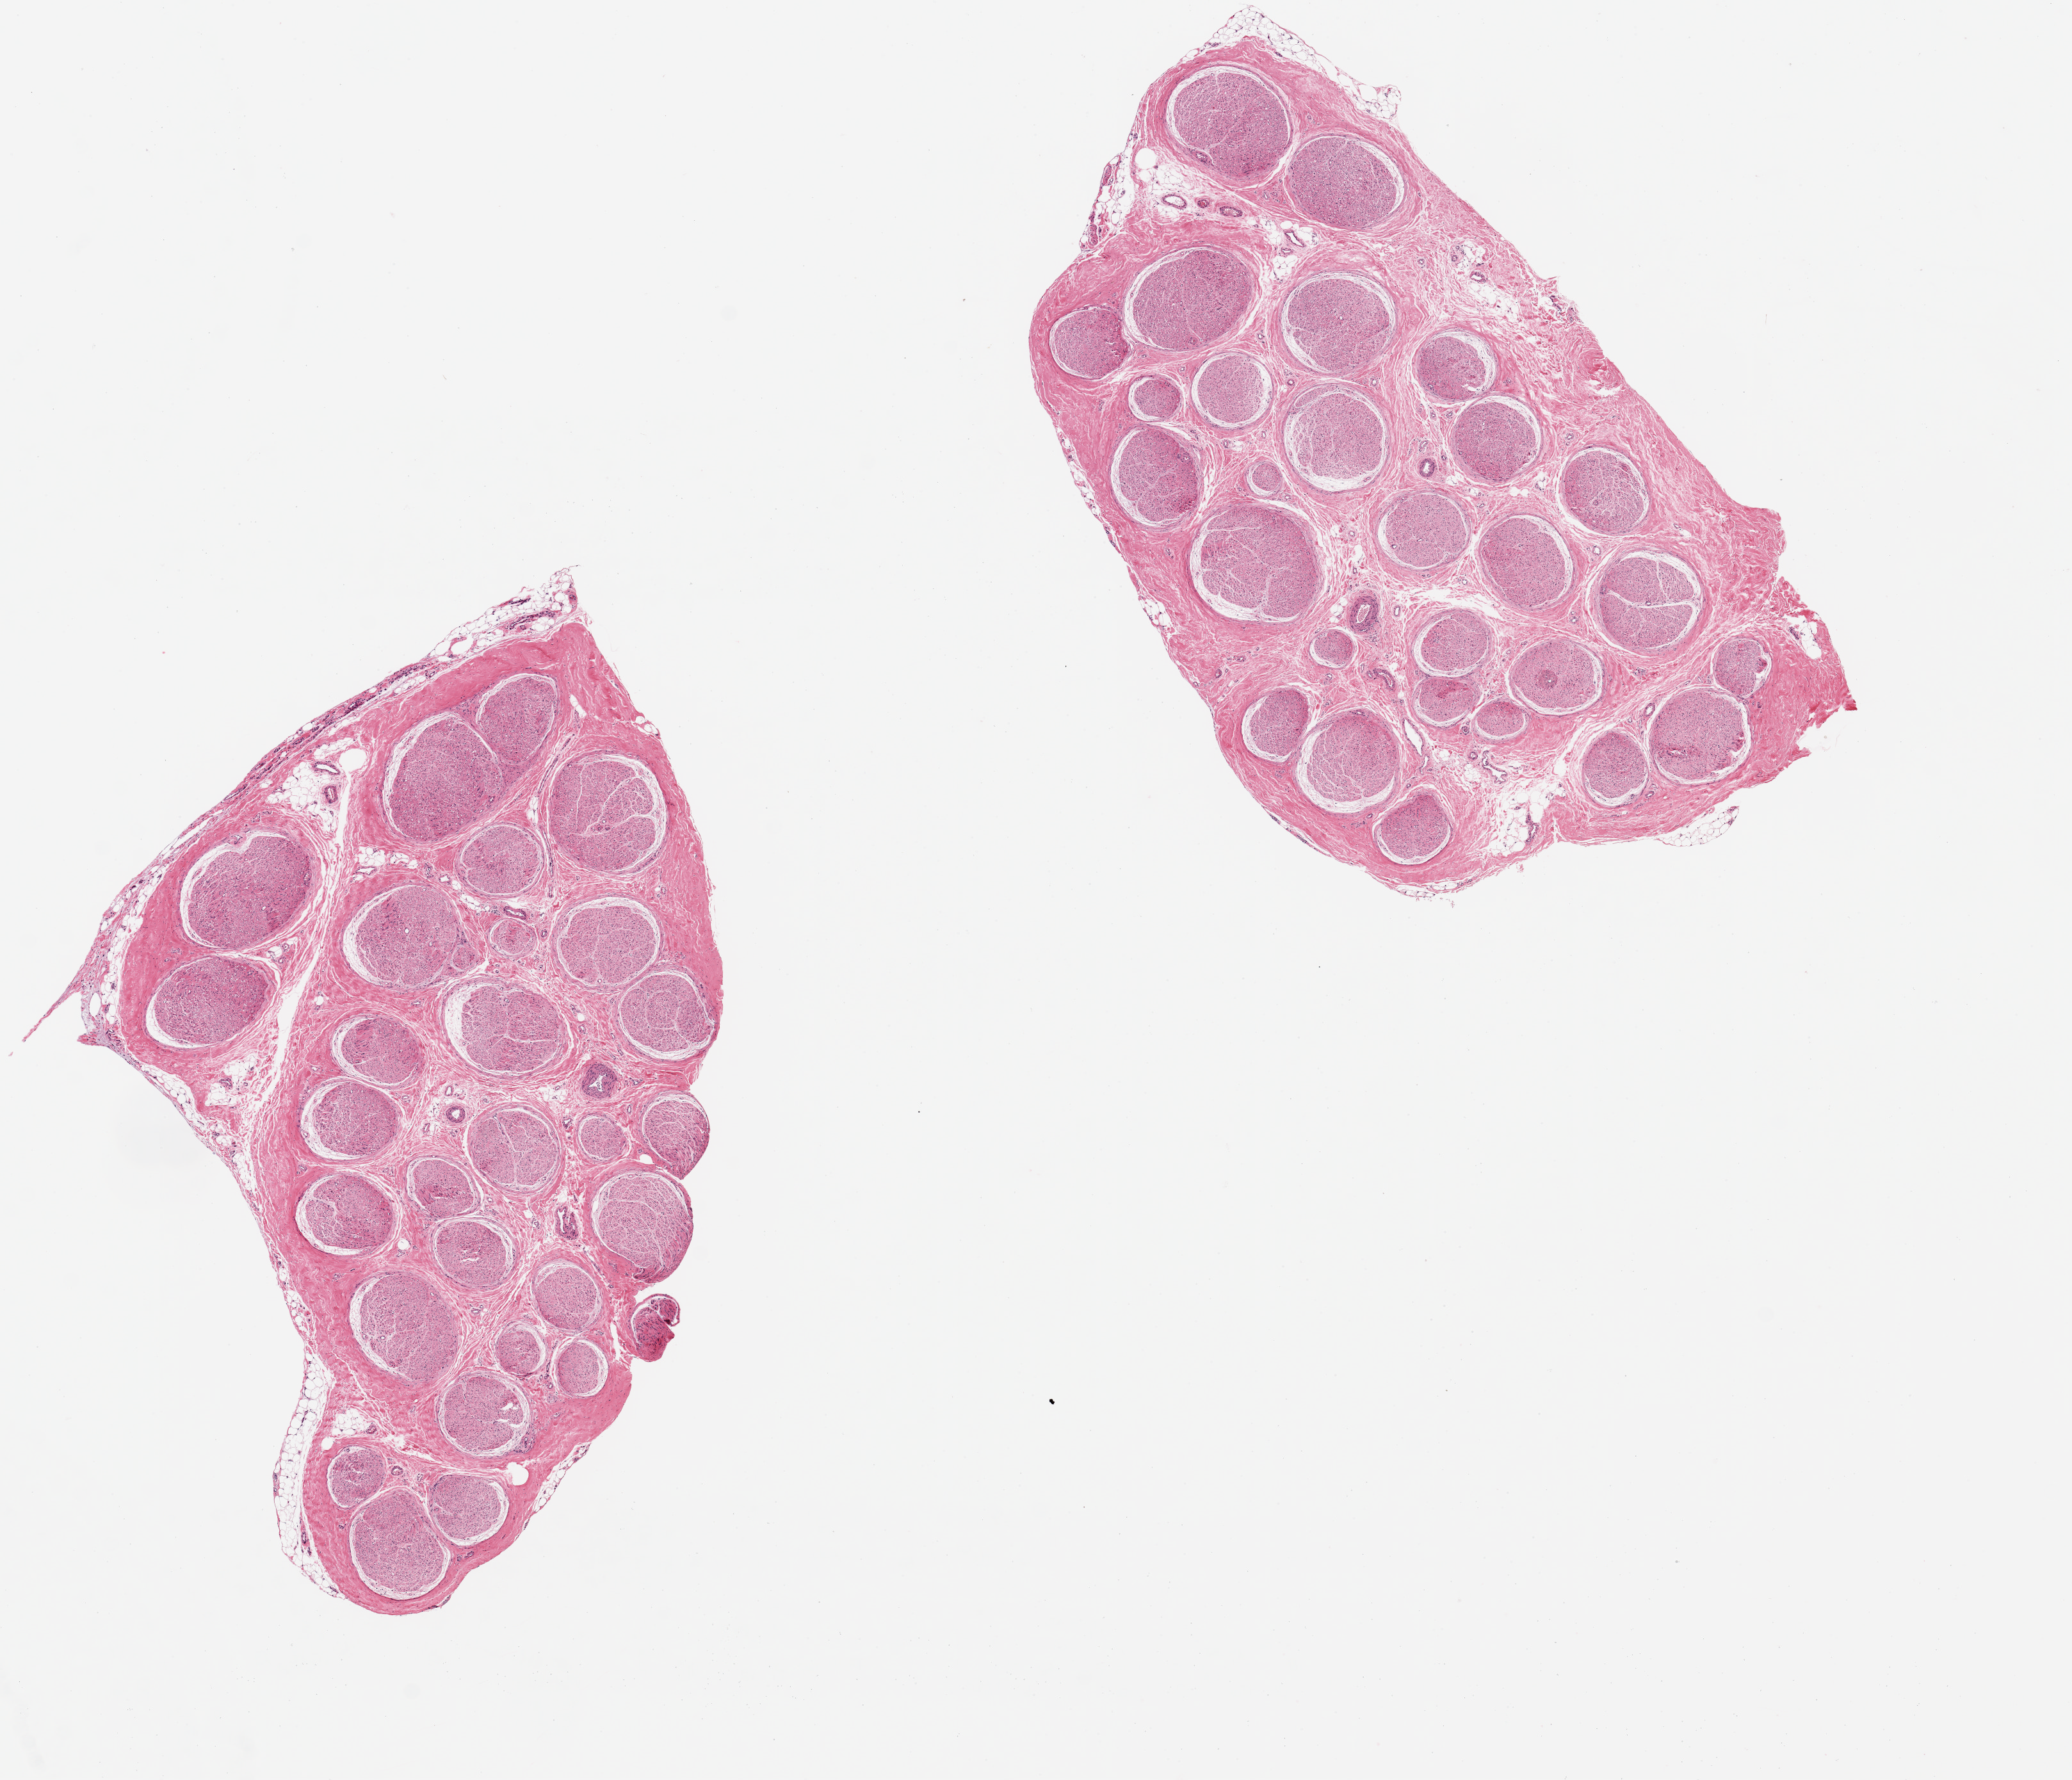
Digitized H&E-stained section, brightfield — shown as a low-resolution overview of the whole scanned area (about 12.8 x 11.0 mm, from a 20x scan); PAXgene-fixed paraffin-embedded (PFPE) section; sampled site (target tissue): tibial nerve; donor tissue sample.
* reviewer comment on this tissue sample: 2 pieces, ~6x3 mm, <2% fat